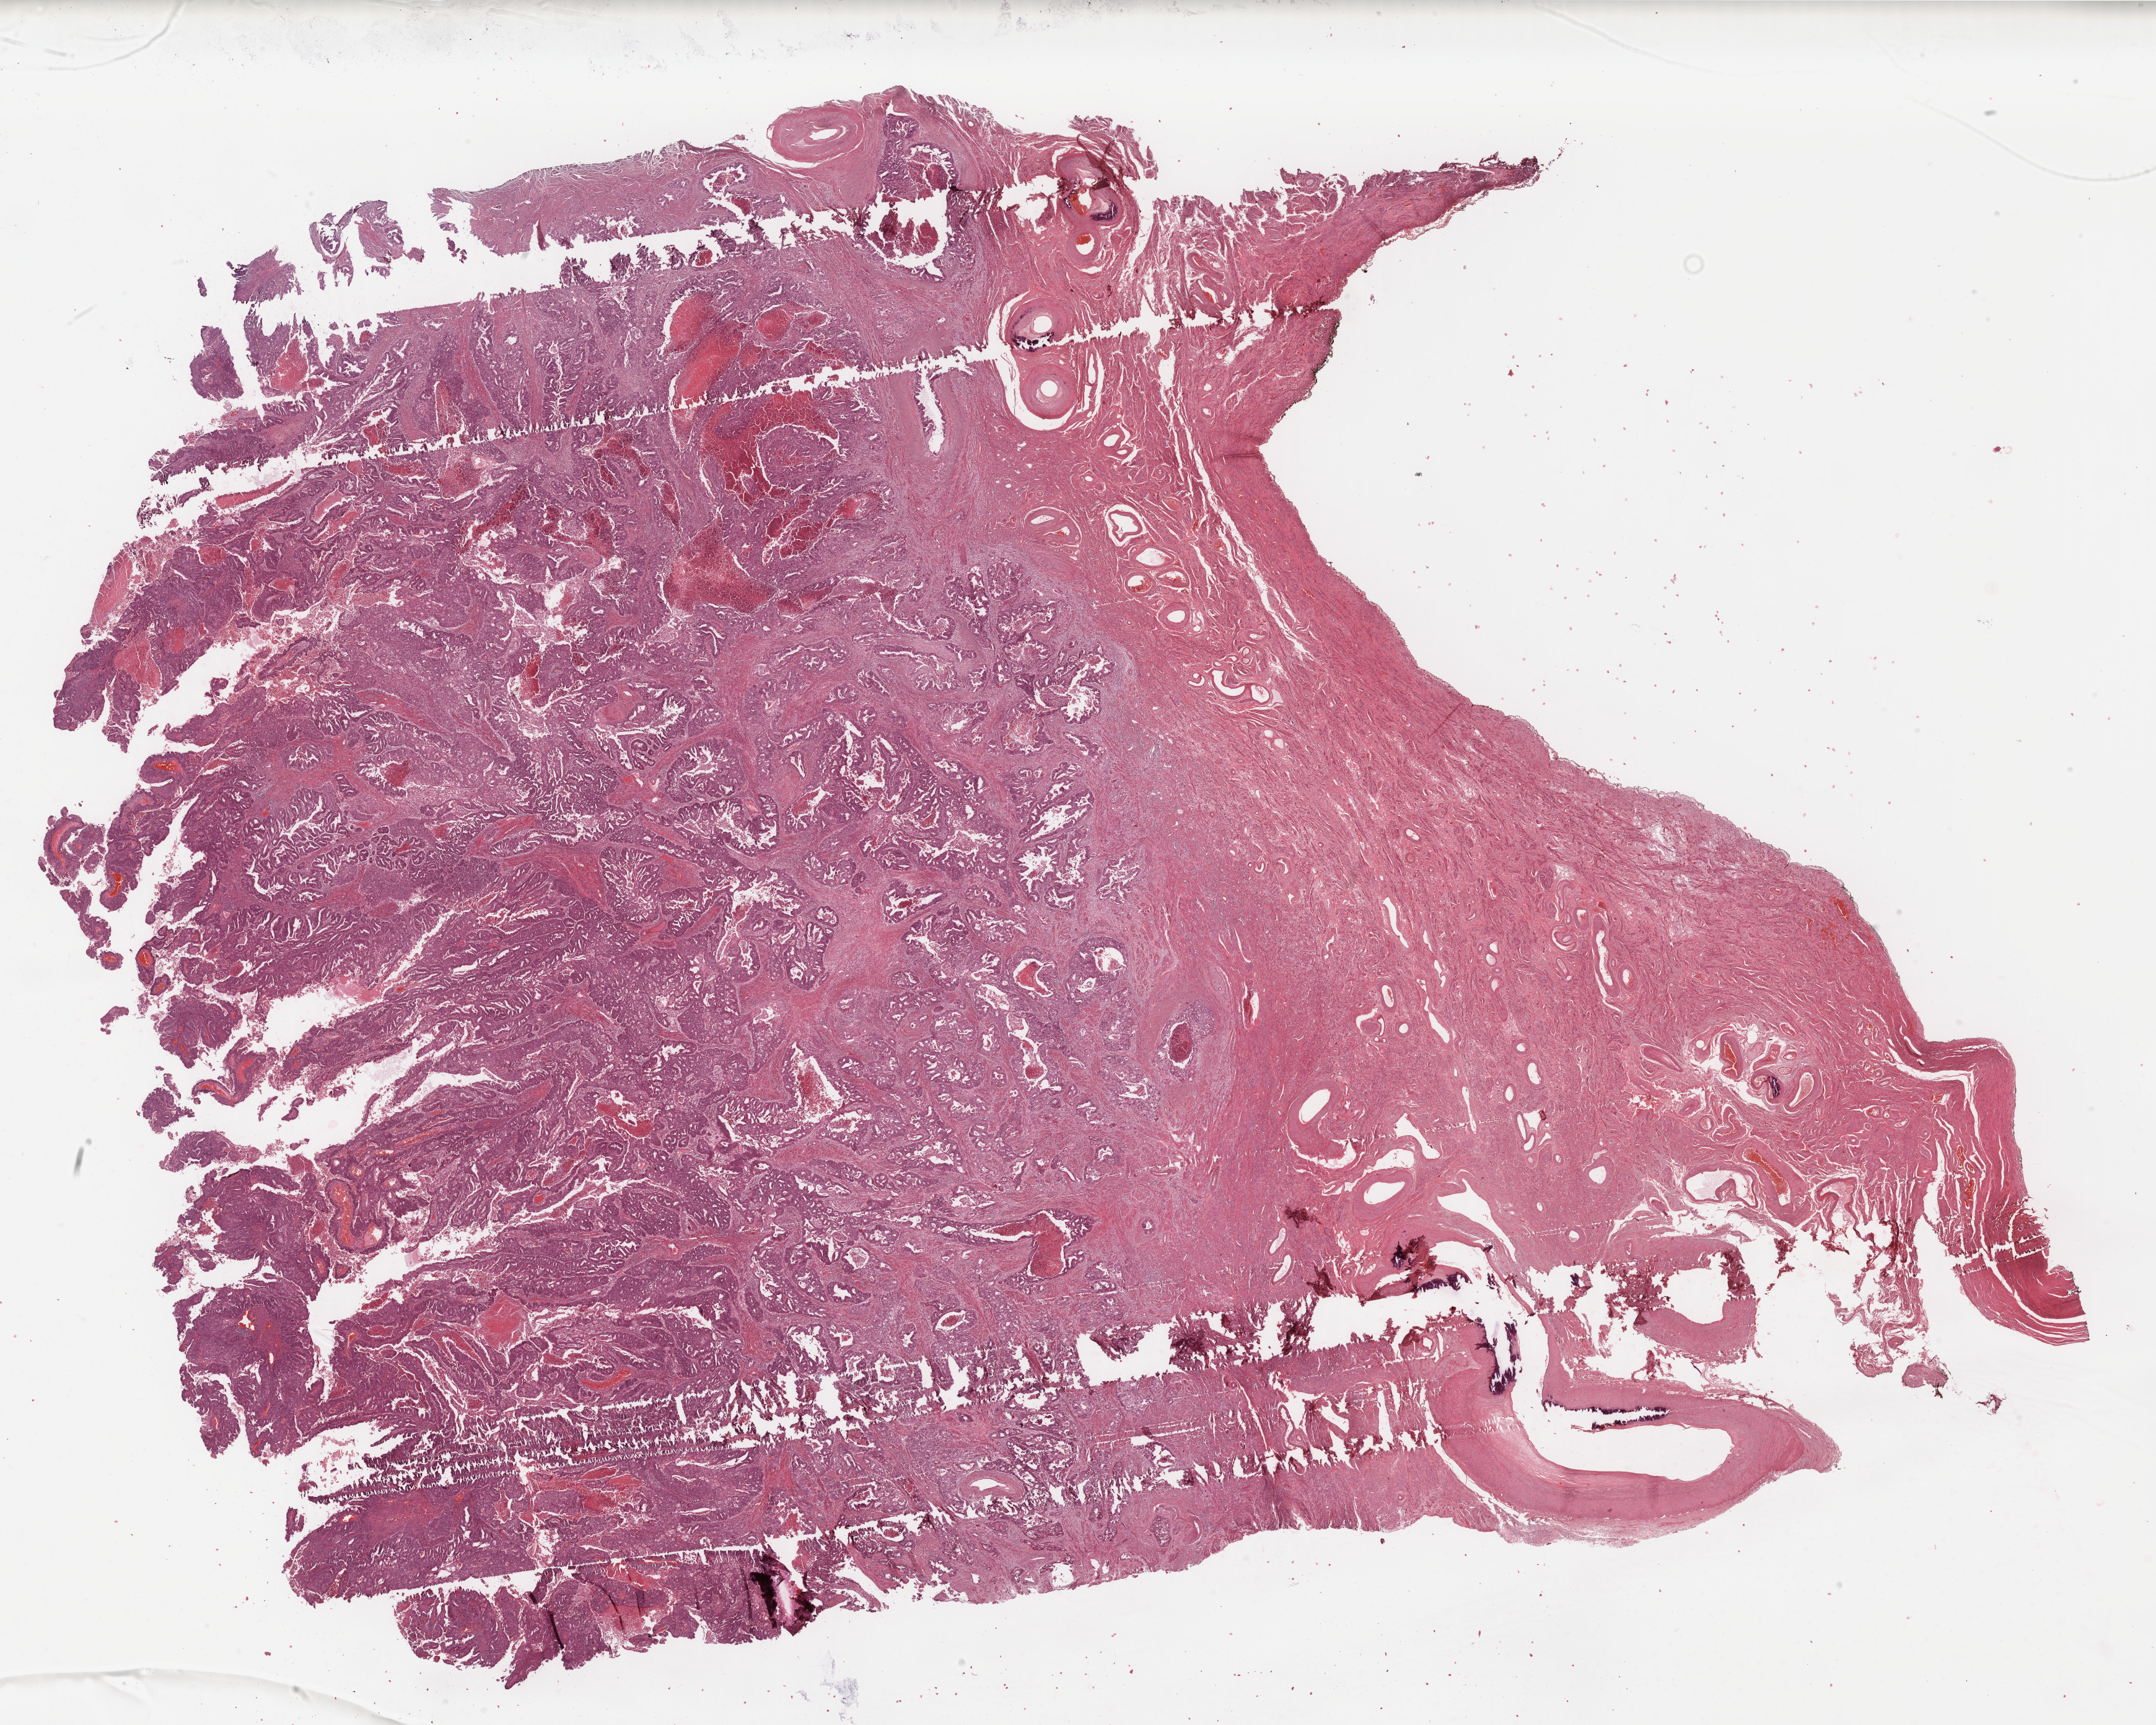
Whole-slide histology image, H&E-stained — a low-resolution overview of the entire scanned area, about 27.6 x 22.1 mm, formalin-fixed paraffin-embedded (FFPE) diagnostic section, primary tumour sample from the uterus. Female patient; age at initial diagnosis 68 years. Histologic grade: G2 (moderately differentiated).
FIGO stage: IIB. Diagnosis: Endometrioid adenocarcinoma, NOS.